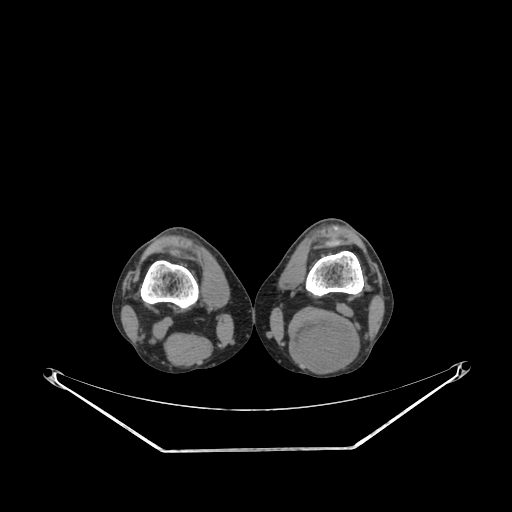
CT of an extremity soft-tissue mass (from a PET/CT study), one axial slice. Position 188 of 267 along the scan axis. Soft-tissue window (W 400 / L 40 HU). 3.75 mm slice thickness. 512 × 512 image matrix. Male patient. Case-level facts recorded for this patient, not image findings: histological type: synovial sarcoma; site of the primary tumour: left poplietal fossa.
Outlined on this slice (expert contour drawn on MRI and transferred to this co-registered scan by the dataset authors):
- gross tumour volume (mass): box from (x=288, y=315) to (x=360, y=373) px